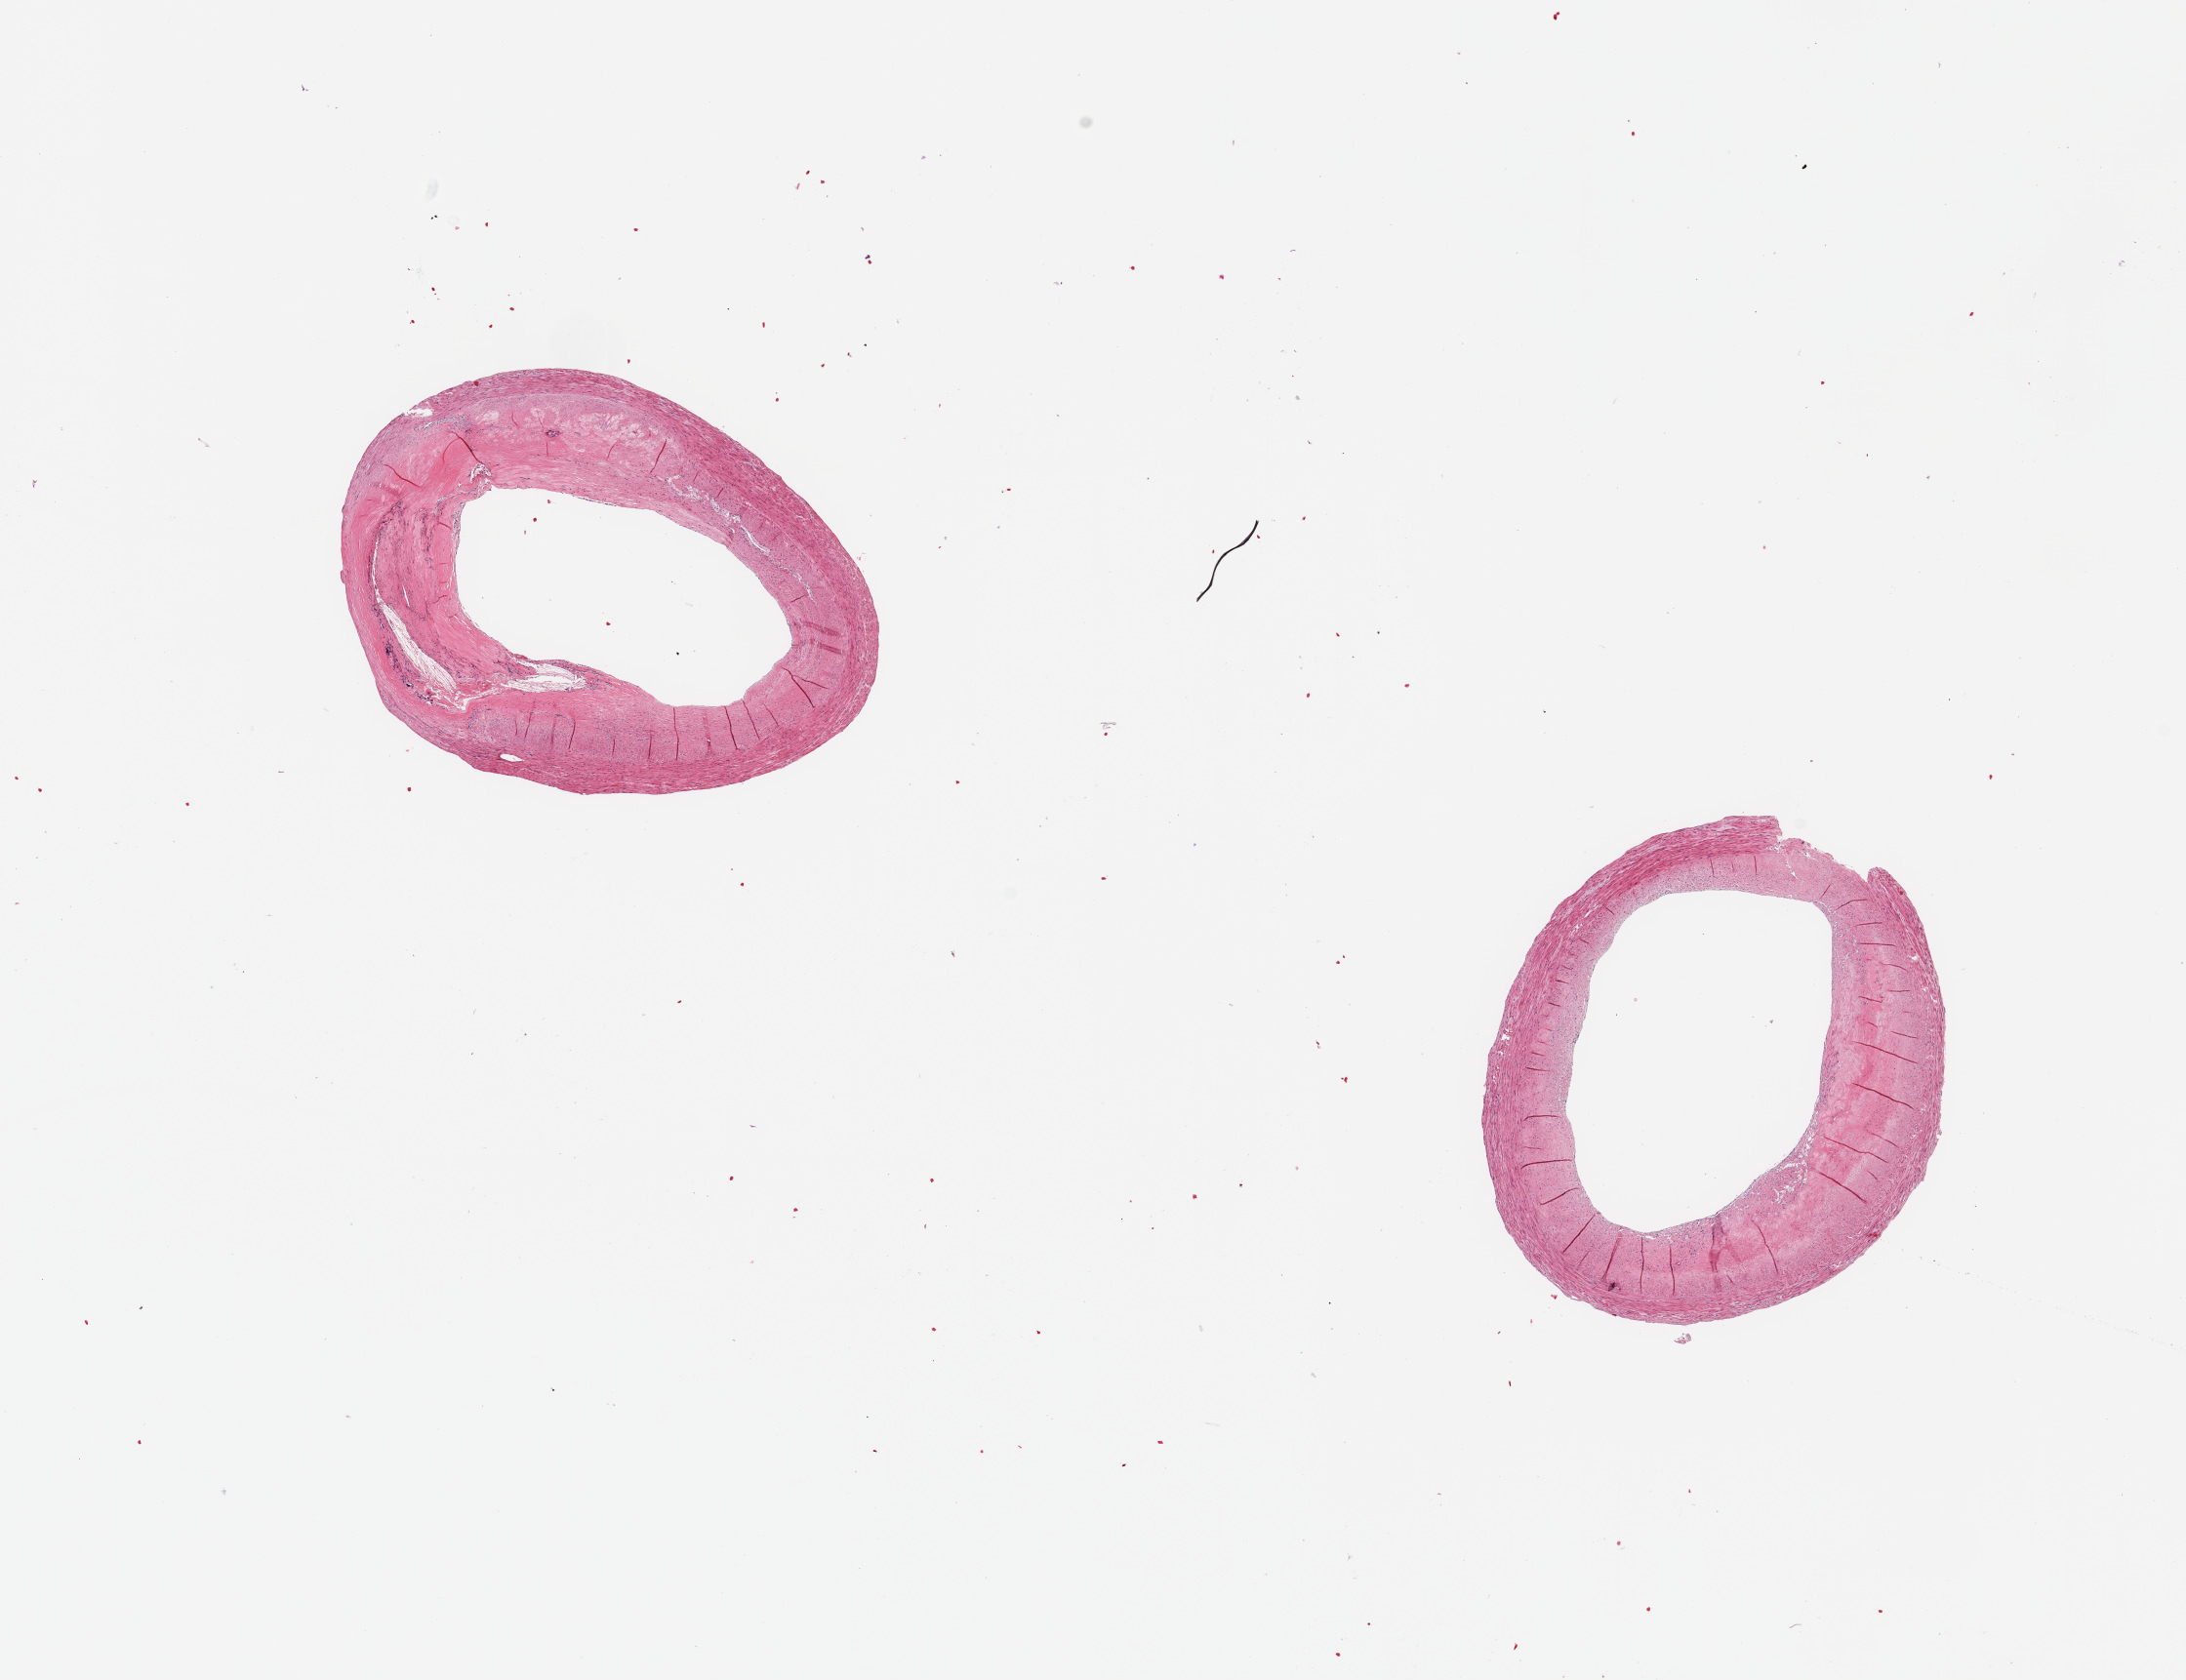
Hematoxylin and eosin (H&E) whole-slide image, shown as a low-resolution overview of the whole scanned area (about 17.7 x 13.6 mm, slide scanned at 20x). PAXgene-fixed paraffin-embedded (PFPE) section. Sampled site (target tissue): coronary artery. Tissue donor sample. Male donor.
Pathologist's review note for this sample: 2 pieces, 30-40% occlusive atherosis.